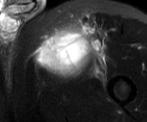
MRI of an extremity soft-tissue mass, one axial slice. Position 48 of 52 along the scan axis. T2-weighted fat-saturated. MR volume resampled by the dataset authors to the PET/CT grid (not the native acquisition matrix). 147 × 122 image matrix, field of view 144 × 119 mm. Male patient. From the clinical record (not read from this slice): histological type: pleiomorphic liposarcoma; grade: high; site of the primary tumour: left thigh.
Outlined on this slice (expert contour drawn on MRI and transferred to this co-registered scan by the dataset authors):
- gross tumour volume including surrounding oedema: bounding box <39,25,104,74> (left, top, right, bottom; pixels)
- gross tumour volume (mass): <39,32,86,68>